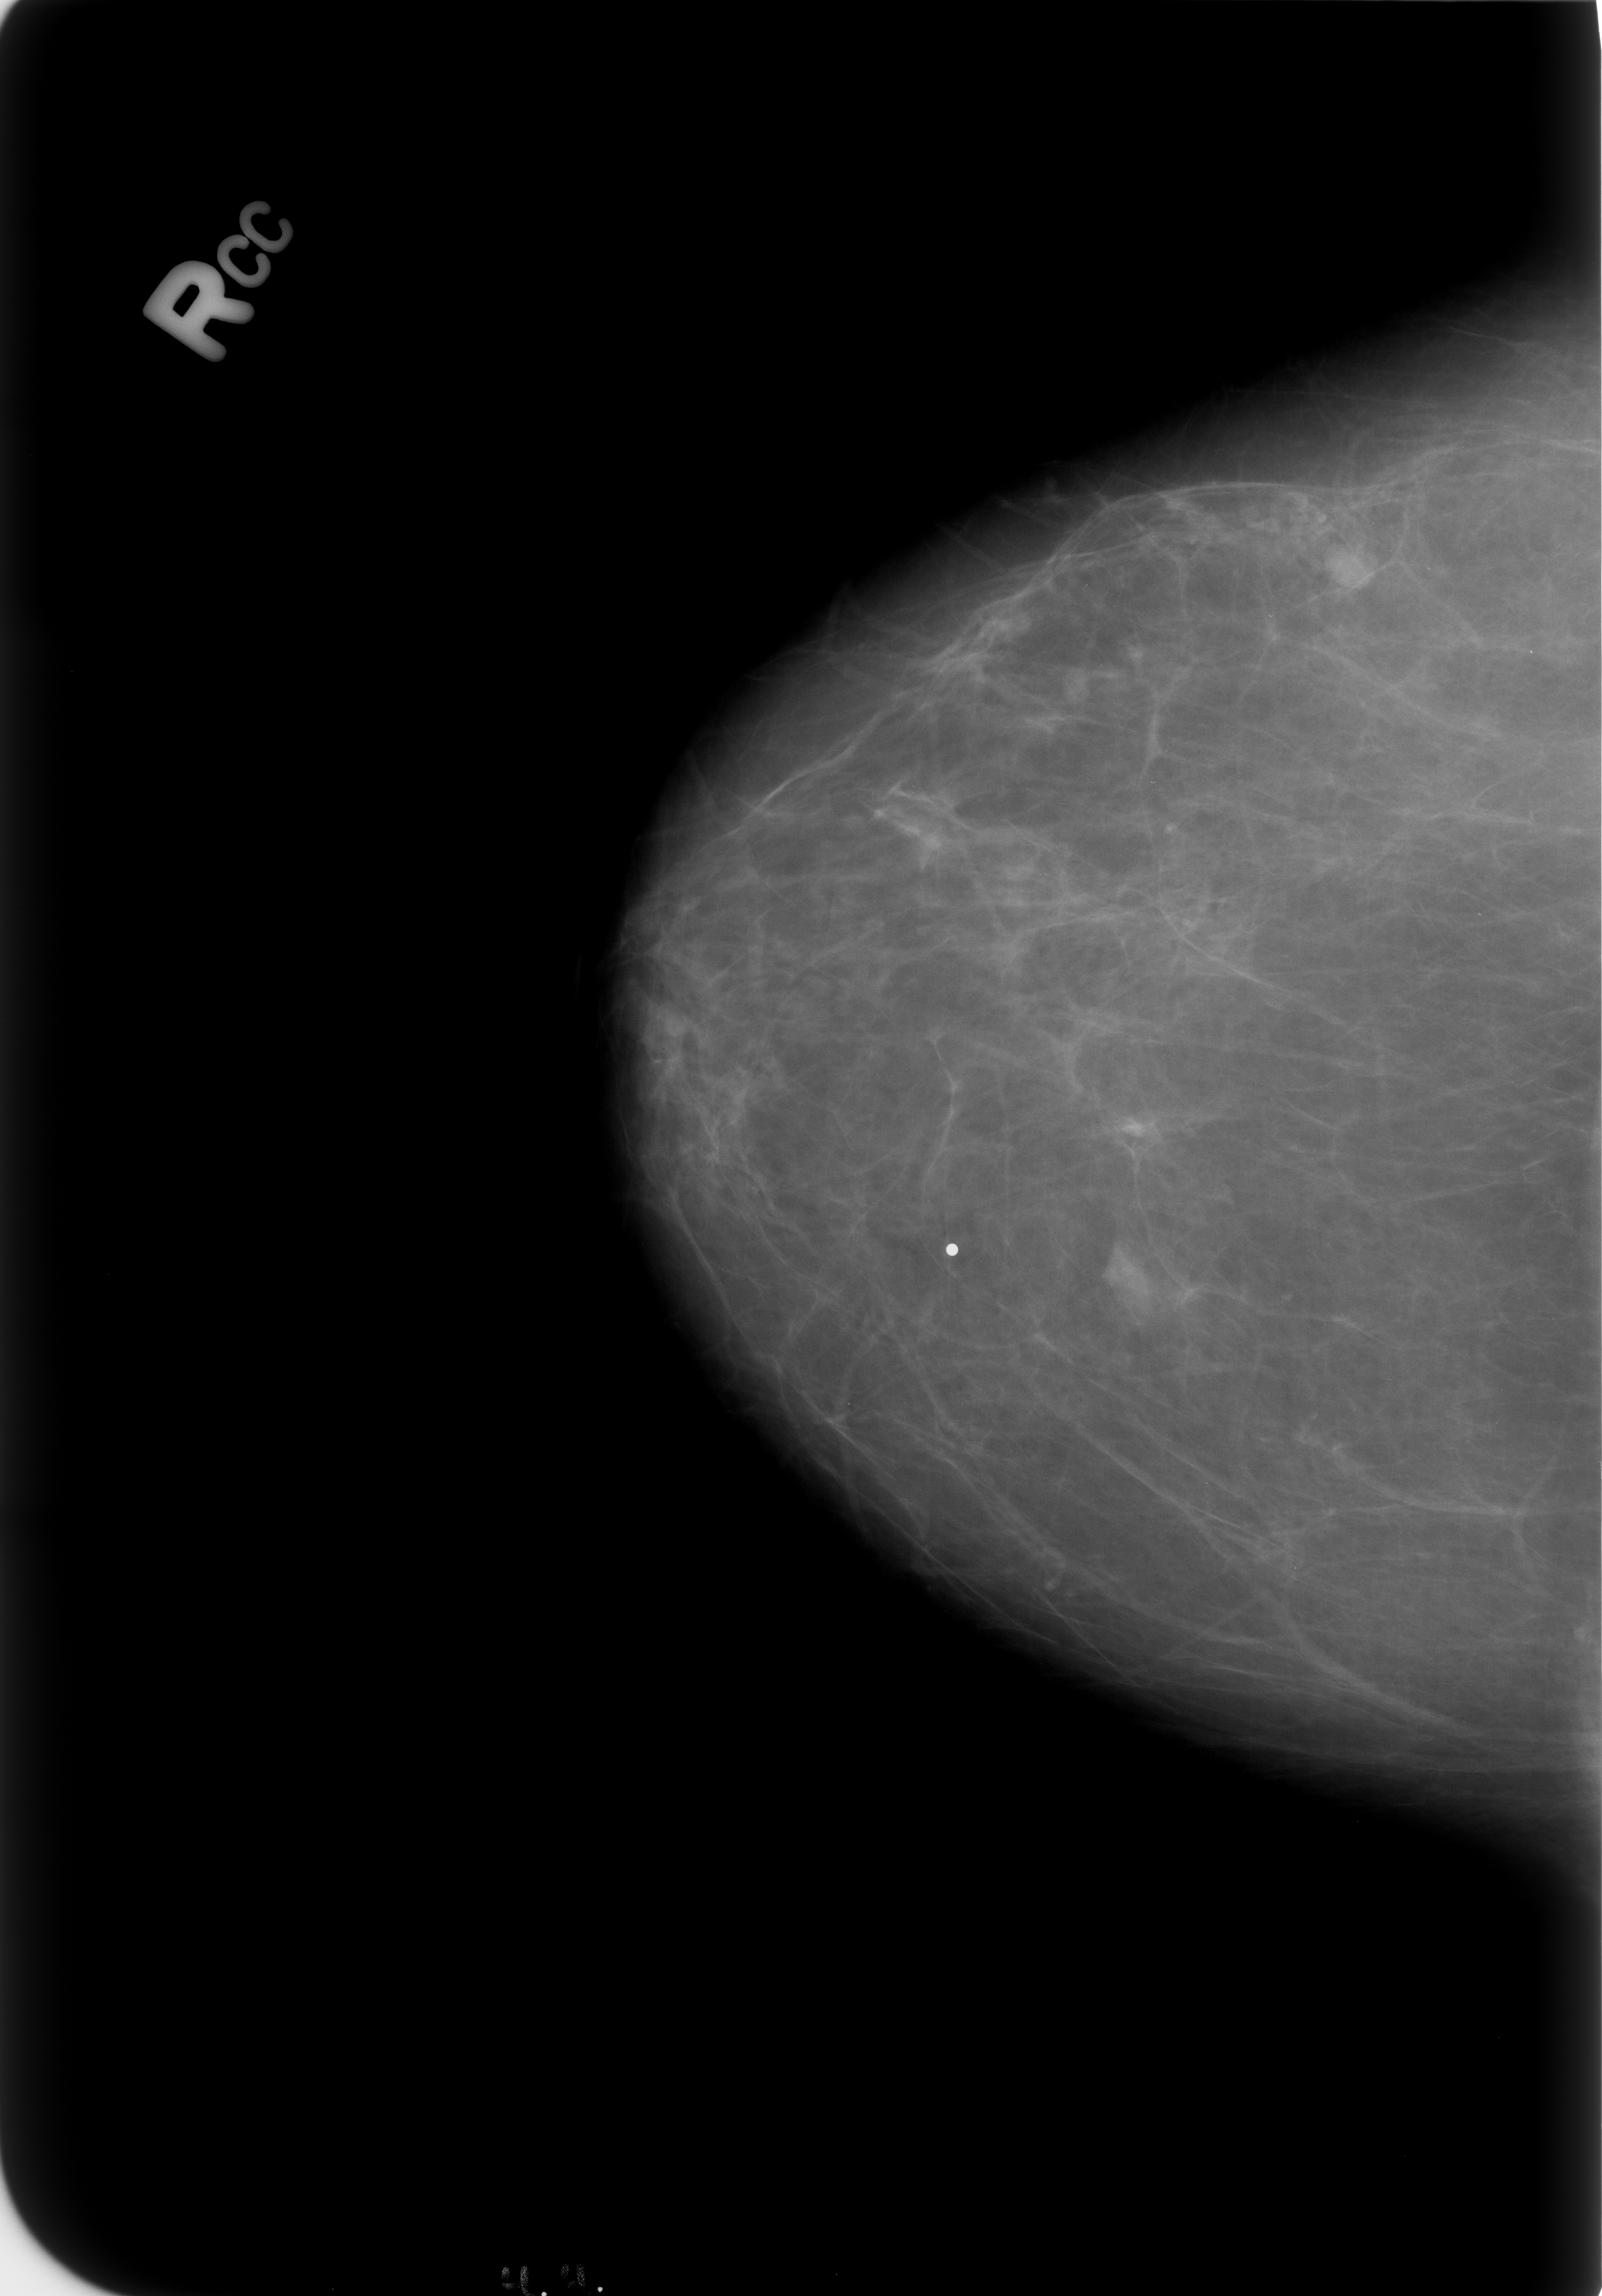
Mammogram (digitized film), right breast, craniocaudal (CC) view.
Mass, shape lymph node; BI-RADS assessment category 2; subtlety rating 3 on a 1 (subtle) to 5 (obvious) scale; benign; no additional work-up was recommended (benign without callback).